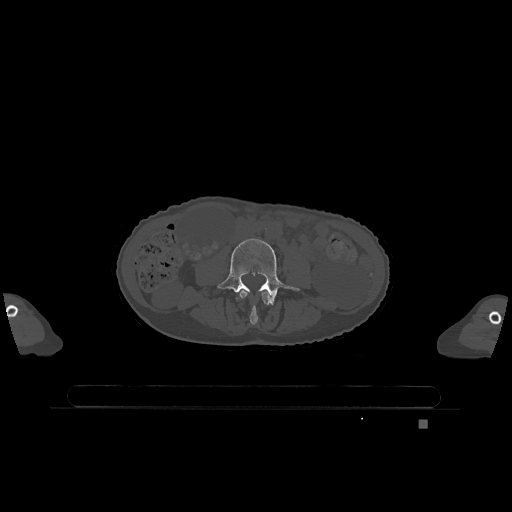
CT including the spine, one axial slice; position 310 of 1317 along the scan axis; bone window (W 1800 / L 400 HU); 0.5 mm slice thickness; 512 × 512 image matrix, field of view 500 × 500 mm. Female patient, age 74 years. Case-level facts recorded for this patient, not image findings: primary cancer: lung; vertebrae with lytic lesions (as recorded): T1, T4, T5, T6, L4, L5.
Annotated regions visible in this slice (semi-automatically segmented with operator editing):
- L3 vertebra: bounding box <239,290,271,325> (left, top, right, bottom; pixels)
- L4 vertebra: <217,238,299,305>